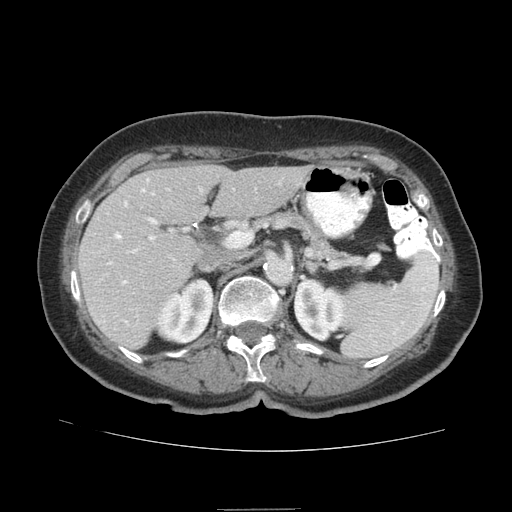
Contrast-enhanced abdominal CT (liver protocol), one axial slice. Position 43 of 95 along the scan axis. 140 kVp. Soft-tissue window (W 400 / L 40 HU). 2.5 mm slice thickness. 512 × 512 image matrix, field of view 360 × 360 mm. From the clinical record (not read from this slice): diagnosis: hepatocellular carcinoma (patient treated with transarterial chemoembolisation; whether this scan precedes or follows treatment is not stated here); TNM stage (as recorded): Stage-IVA; Child-Pugh class: B; tumour differentiation: moderately differentiated; tumour nodularity: uninodular.
Annotated regions visible in this slice (semi-automatic segmentation, software-assisted and operator-edited):
- liver parenchyma outside the tumour (the mass and vessels are separate outlines, so this box may not span the whole liver): box from (x=76, y=164) to (x=311, y=348) px
- liver vessels: (x=109, y=179)–(x=201, y=284)